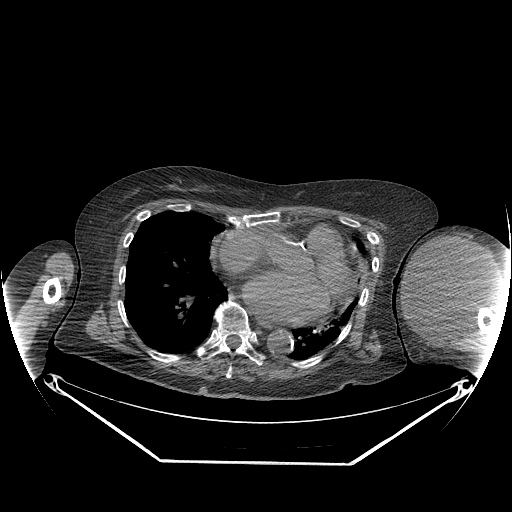
CT of an extremity soft-tissue mass (from a PET/CT study), one axial slice; slice 161 of 267 in the series (ordered by position); 140 kVp; soft-tissue window (W 400 / L 40 HU); 3.75 mm slice thickness; 512 × 512 image matrix, field of view 500 × 500 mm. Female patient. Case-level facts recorded for this patient, not image findings: histological type: pleiomorphic leiomyosarcoma; grade: high; site of the primary tumour: left biceps.
Annotated regions visible in this slice (expert contour drawn on MRI and transferred to this co-registered scan by the dataset authors):
- gross tumour volume including surrounding oedema: box from (x=402, y=235) to (x=492, y=330) px
- gross tumour volume (mass): (x=402, y=237)–(x=492, y=330)